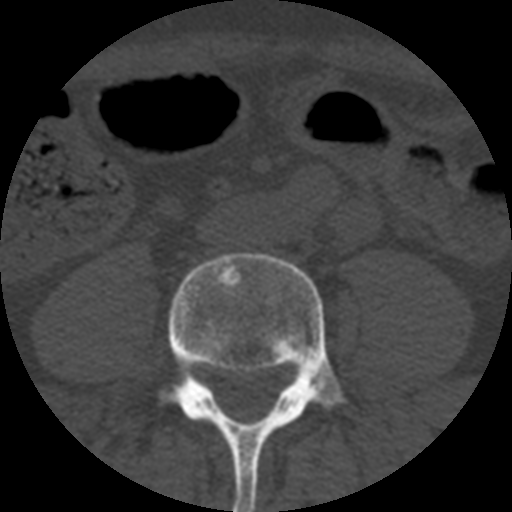
CT including the spine, one axial slice. Slice 90 of 508 in the series (ordered by position). Reconstruction kernel STANDARD. 120 kVp. Bone window (W 1800 / L 400 HU). 1.25 mm slice thickness. 512 × 512 image matrix, field of view 160 × 160 mm. Patient age 57 years. Case-level facts recorded for this patient, not image findings: primary cancer: prostate.
Structures marked on this image (semi-automatic segmentation, software-assisted and operator-edited):
- L4 vertebra: bounding box <156,253,351,512> (left, top, right, bottom; pixels)